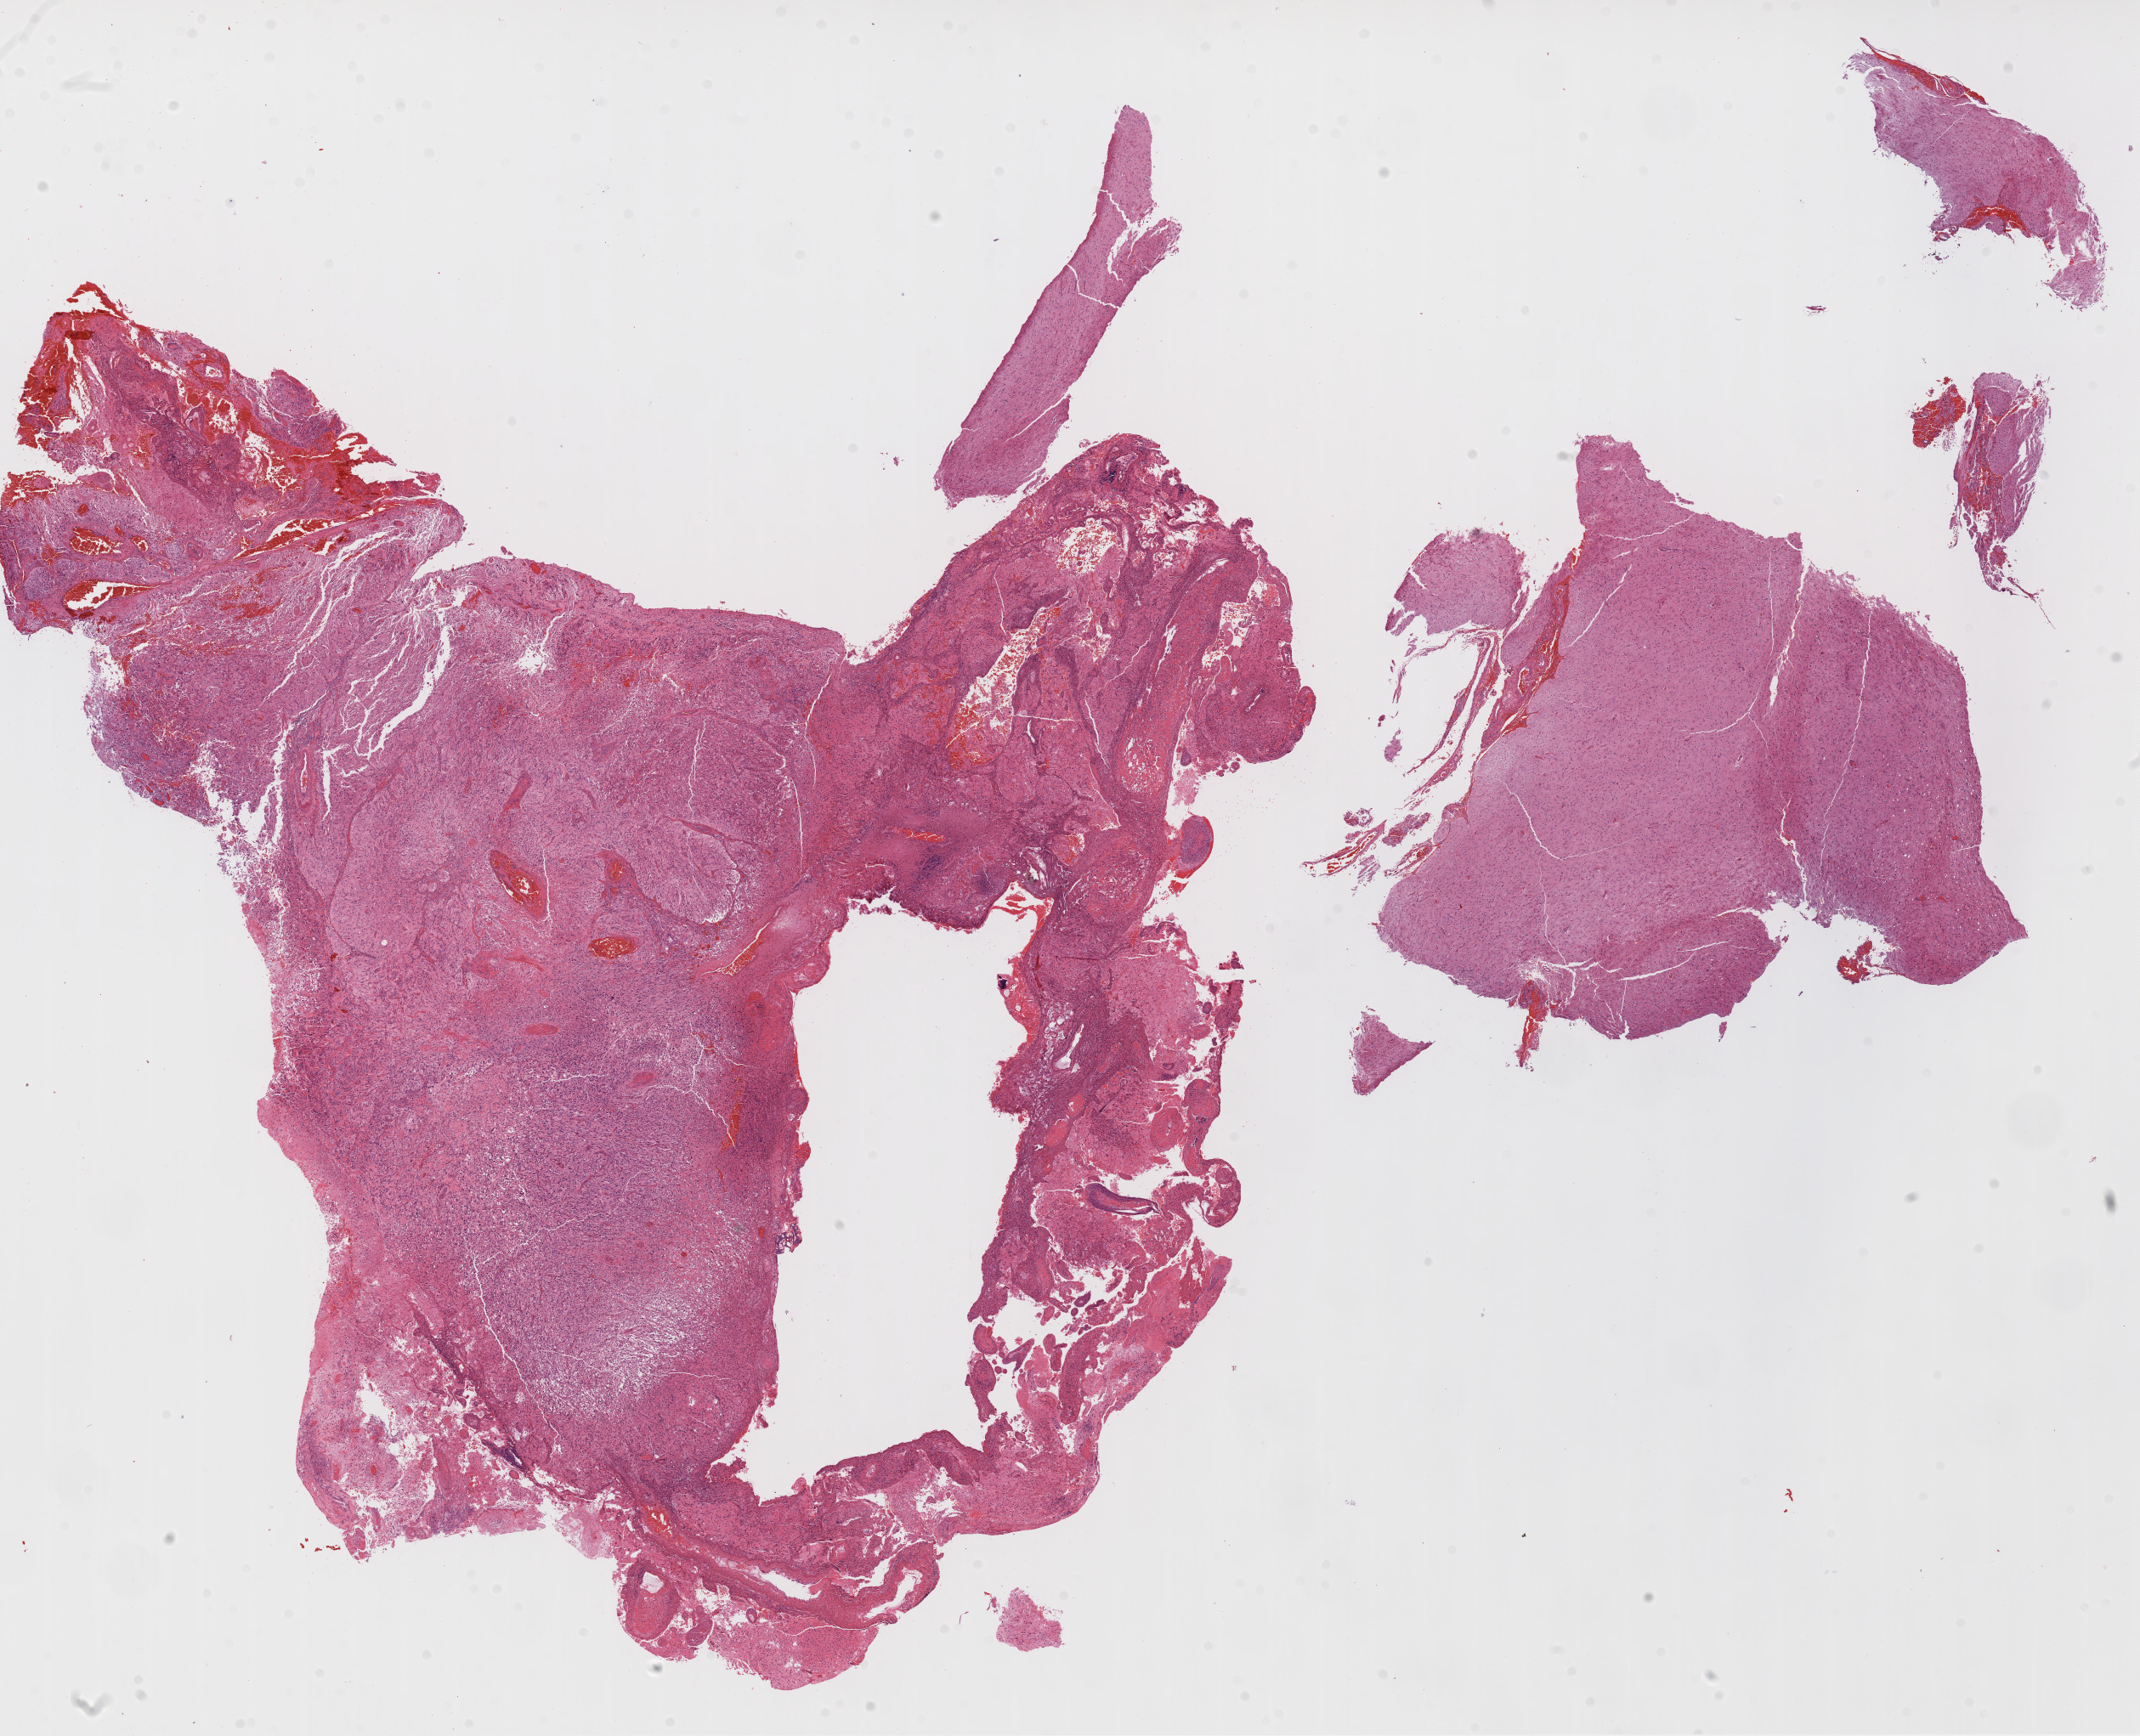
Whole-slide histology image, H&E — a low-resolution overview of the entire scanned area, about 20.3 x 16.5 mm (slide scanned at 20x); formalin-fixed paraffin-embedded (FFPE) diagnostic section; primary tumour sample from the brain. Patient: male, age at initial diagnosis 62 years.
Pathologic diagnosis: Glioblastoma.